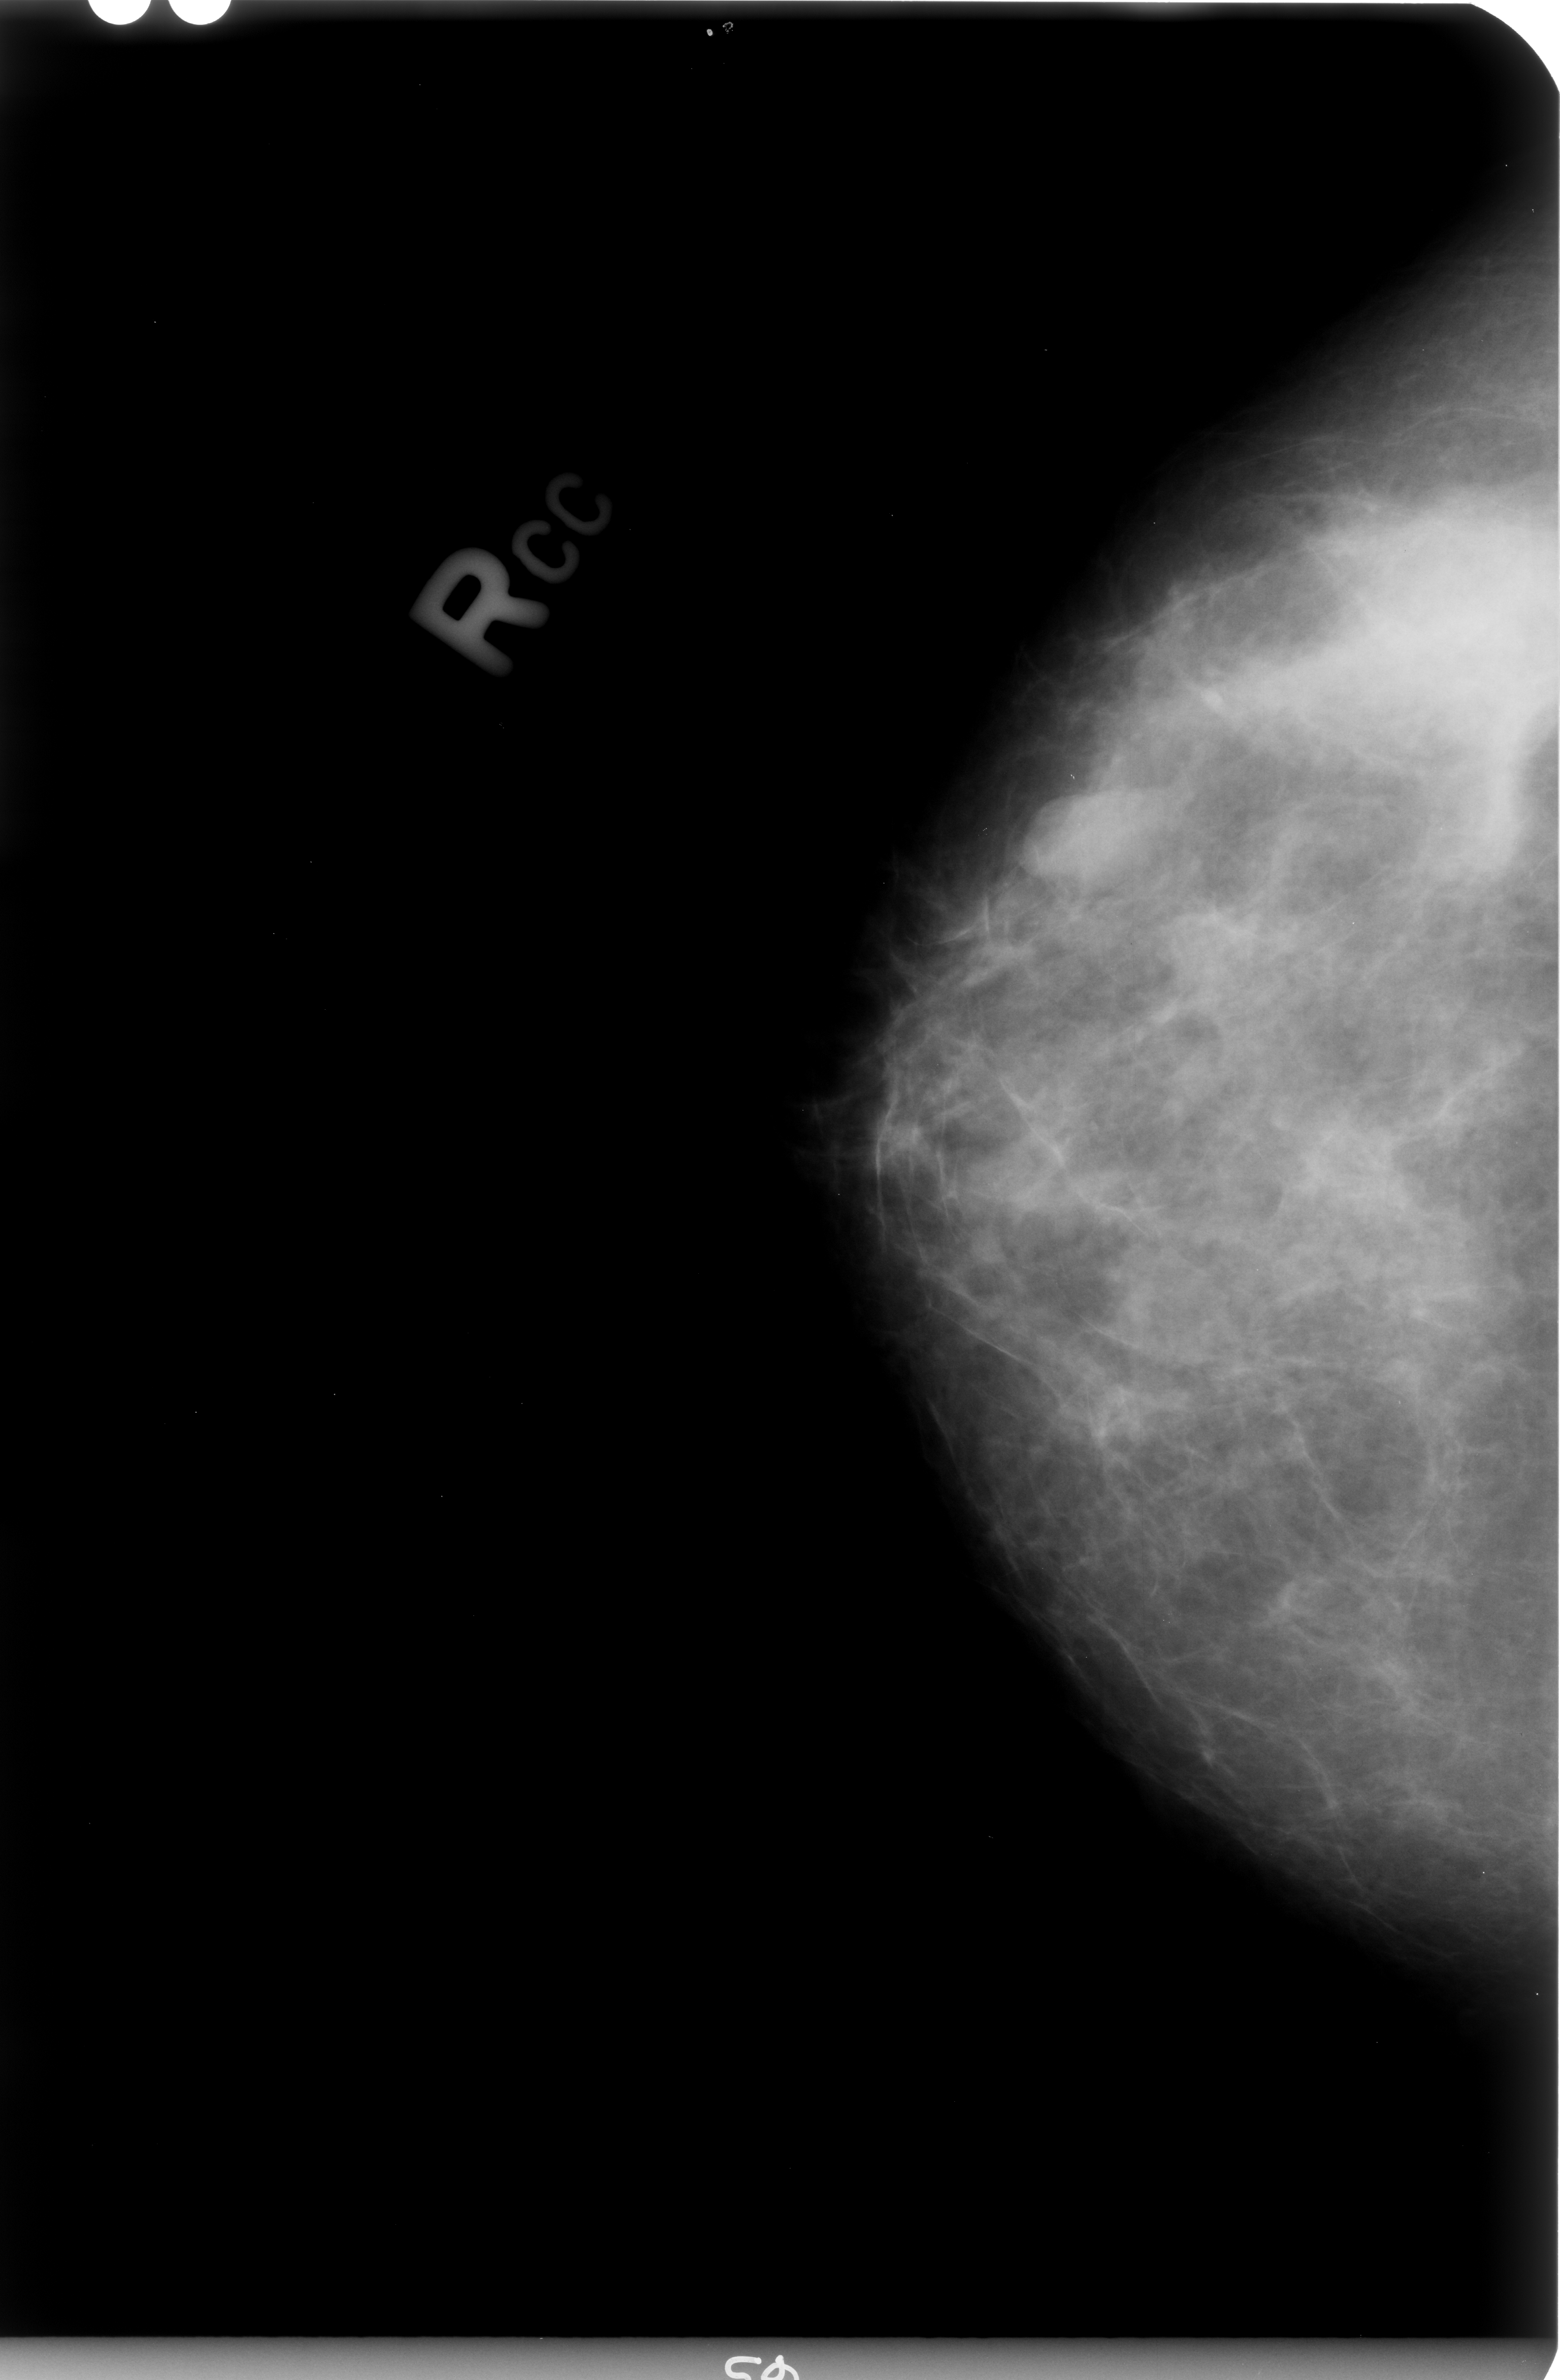
Mammogram (digitized film); right breast; CC view; breast composition: heterogeneously dense (BI-RADS density category 3 of 4); 1560 × 2380 image matrix.
Expert-marked regions of interest on this image (one box per marked abnormality):
- mass, shape lobulated, margins circumscribed / ill defined; BI-RADS assessment category 4; pathology (as recorded): benign: bounding box <1042,775,1156,877> (left, top, right, bottom; pixels)